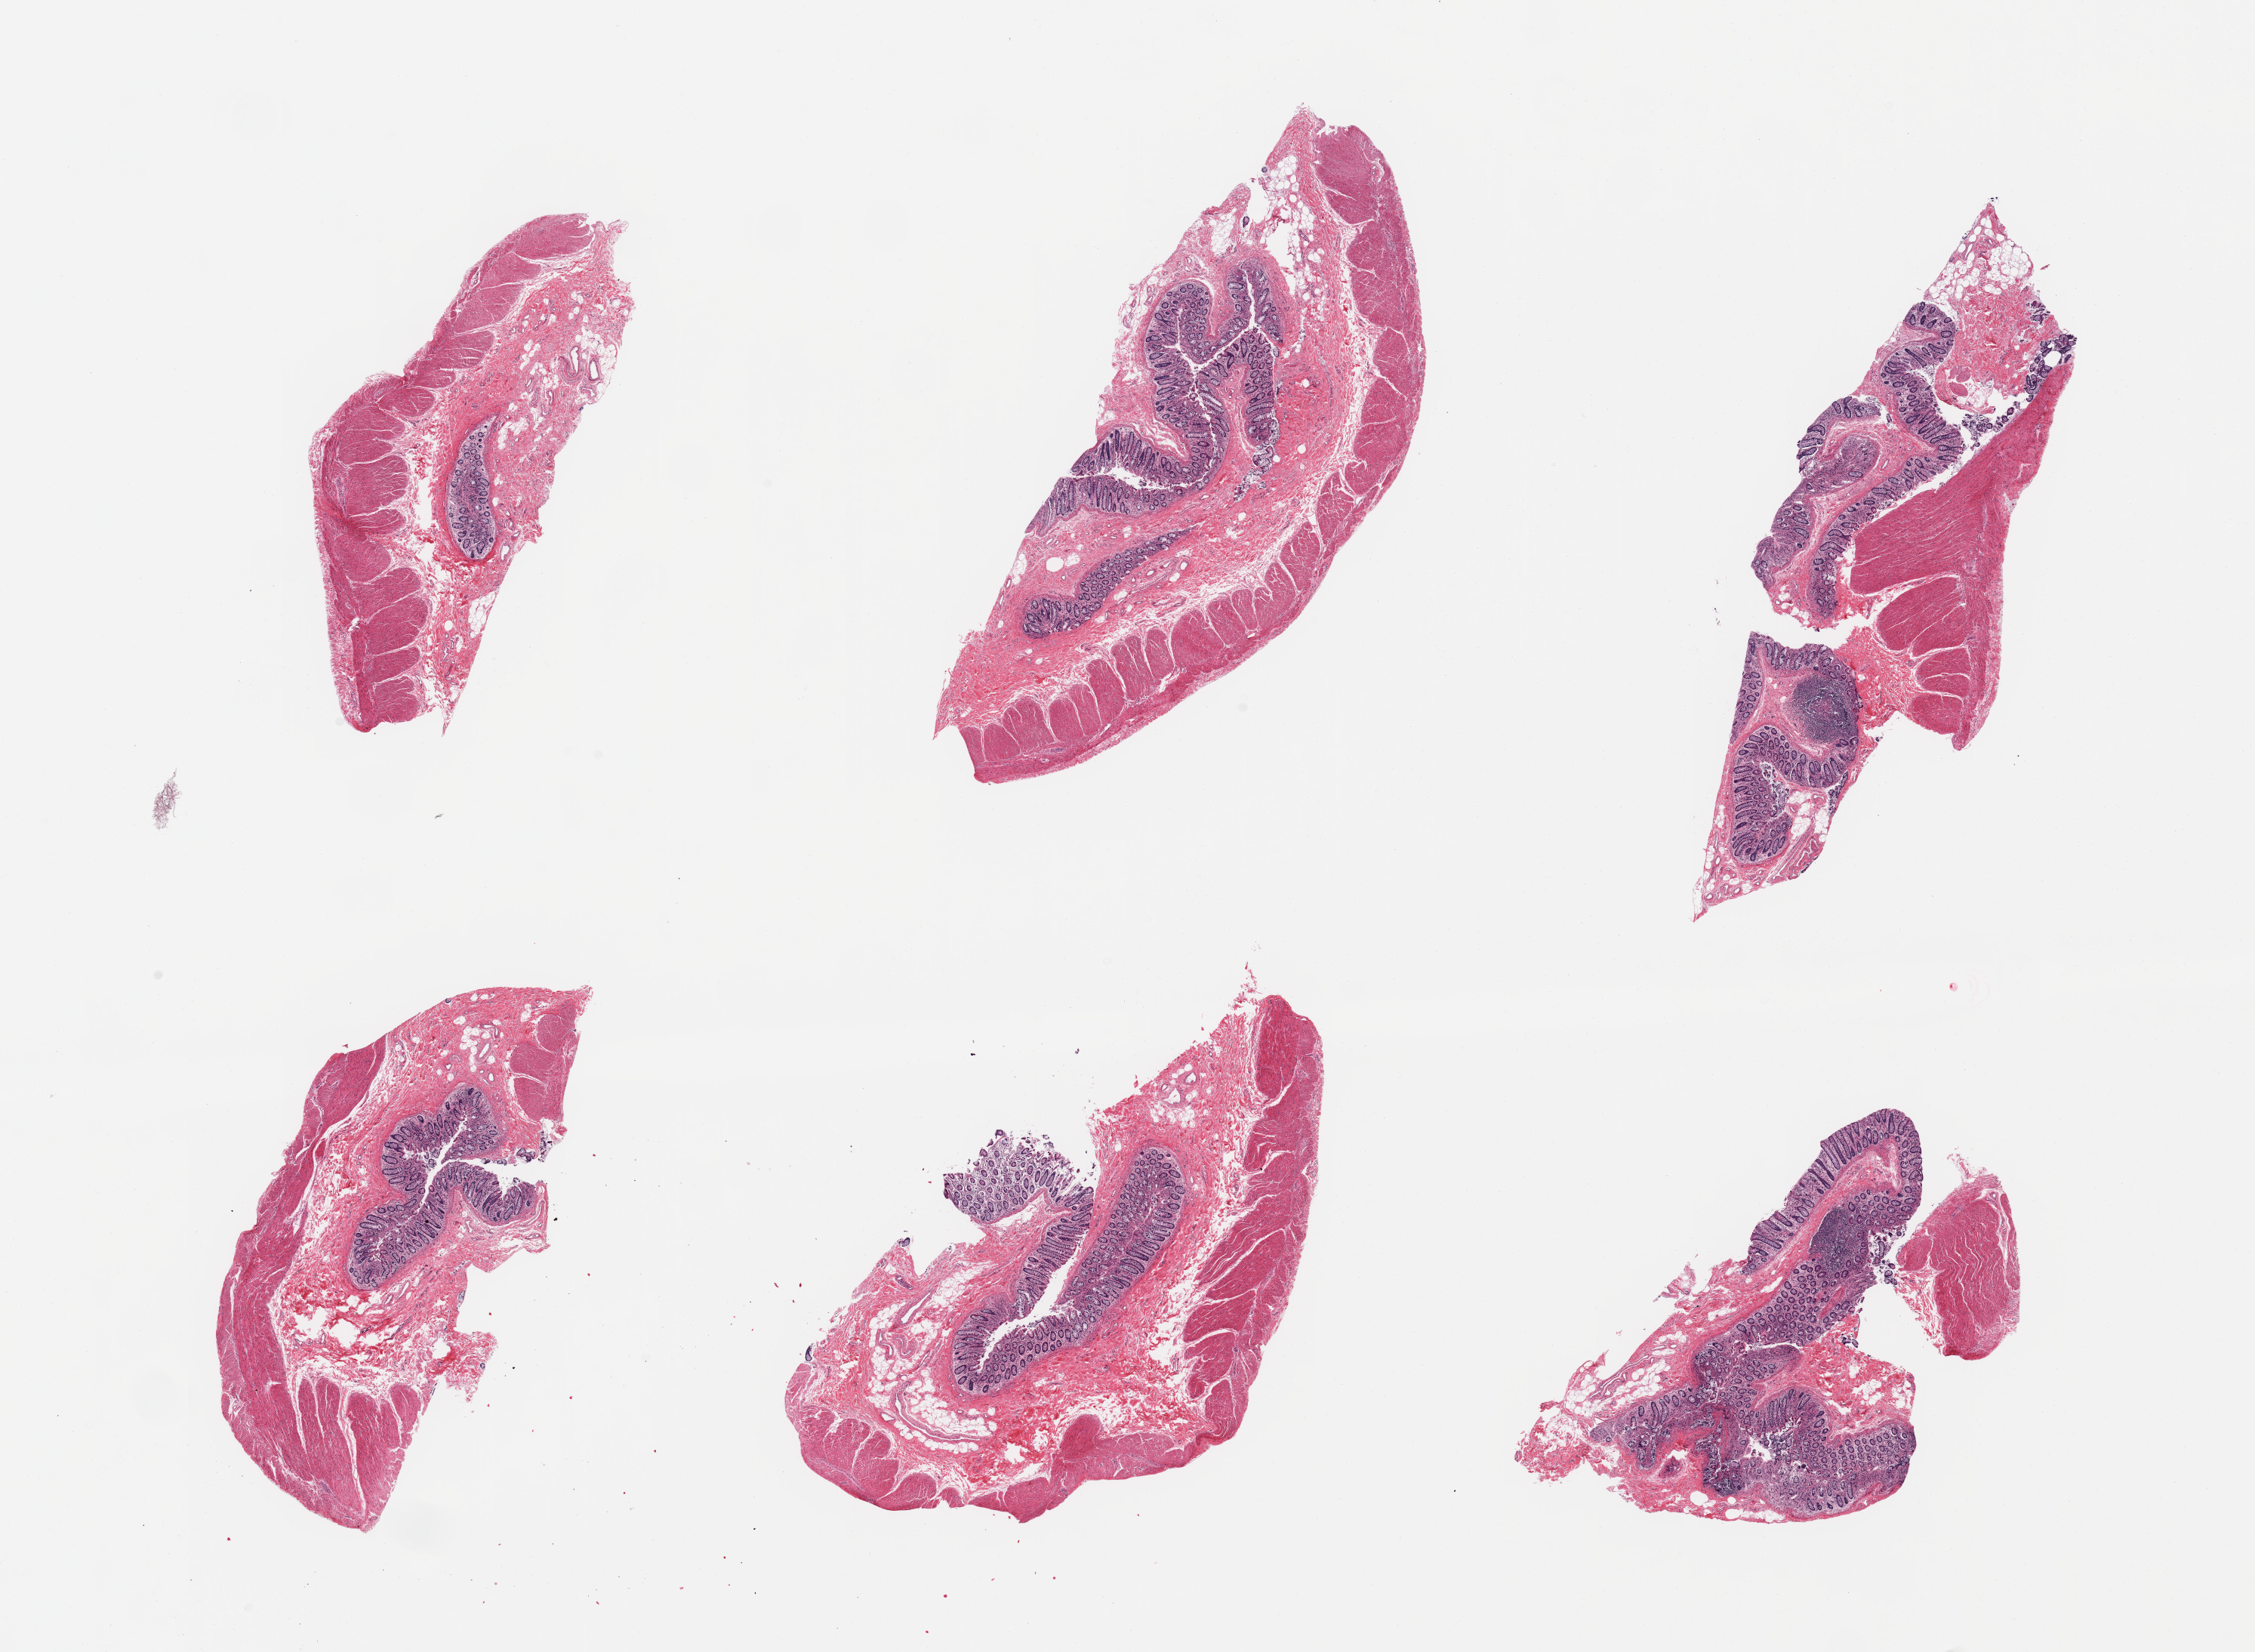
Whole-slide image, hematoxylin and eosin (H&E) stain — low-resolution overview of the scanned area, about 23.6 x 17.3 mm, PAXgene-fixed, paraffin-embedded tissue, sampled site (target tissue): transverse colon, tissue donor sample. Donor sex: male.
Pathologist's review note for this sample: 6 pieces; full thickness sections, mild to moderate mucosal autolysis.